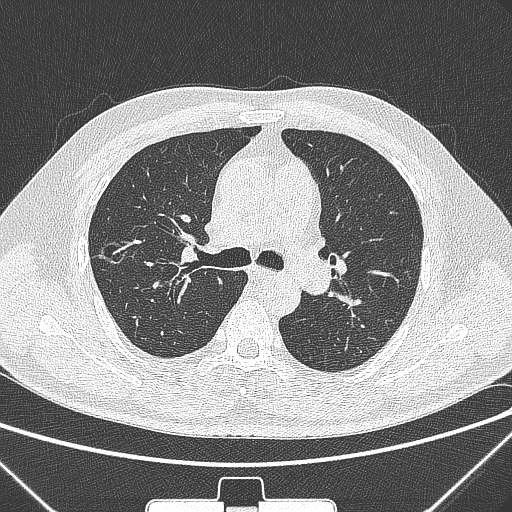
Chest CT, one axial slice. Position 196 of 320 along the scan axis. 120 kVp. Lung window (W 1500 / L -600 HU). 1 mm slice thickness. 512 × 512 image matrix. Male patient, age 58 years. Case-level facts recorded for this patient, not image findings: clinical TNM (as recorded): T1c N0 M0; histopathological grade: G2.
Structures marked on this image (rectangle marked by the reading radiologist):
- lung tumour (recorded histology: adenocarcinoma): bounding box <98,234,131,274> (left, top, right, bottom; pixels)